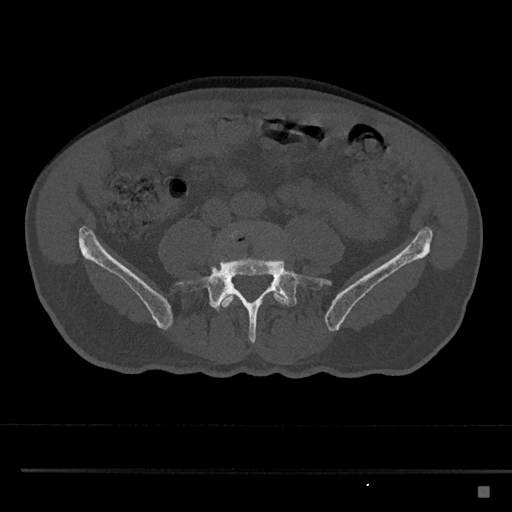
CT including the spine, one axial slice; reconstruction kernel Br40s/3; 120 kVp; bone window (W 1800 / L 400 HU); 512 × 512 image matrix, field of view 391 × 391 mm. Male patient, age 59 years. From the clinical record (not read from this slice): primary cancer: prostate.
Annotated regions visible in this slice (semi-automatically segmented with operator editing):
- L4 vertebra: bounding box [x1, y1, x2, y2] px = [216, 224, 289, 312]
- L5 vertebra: [176, 241, 331, 343]